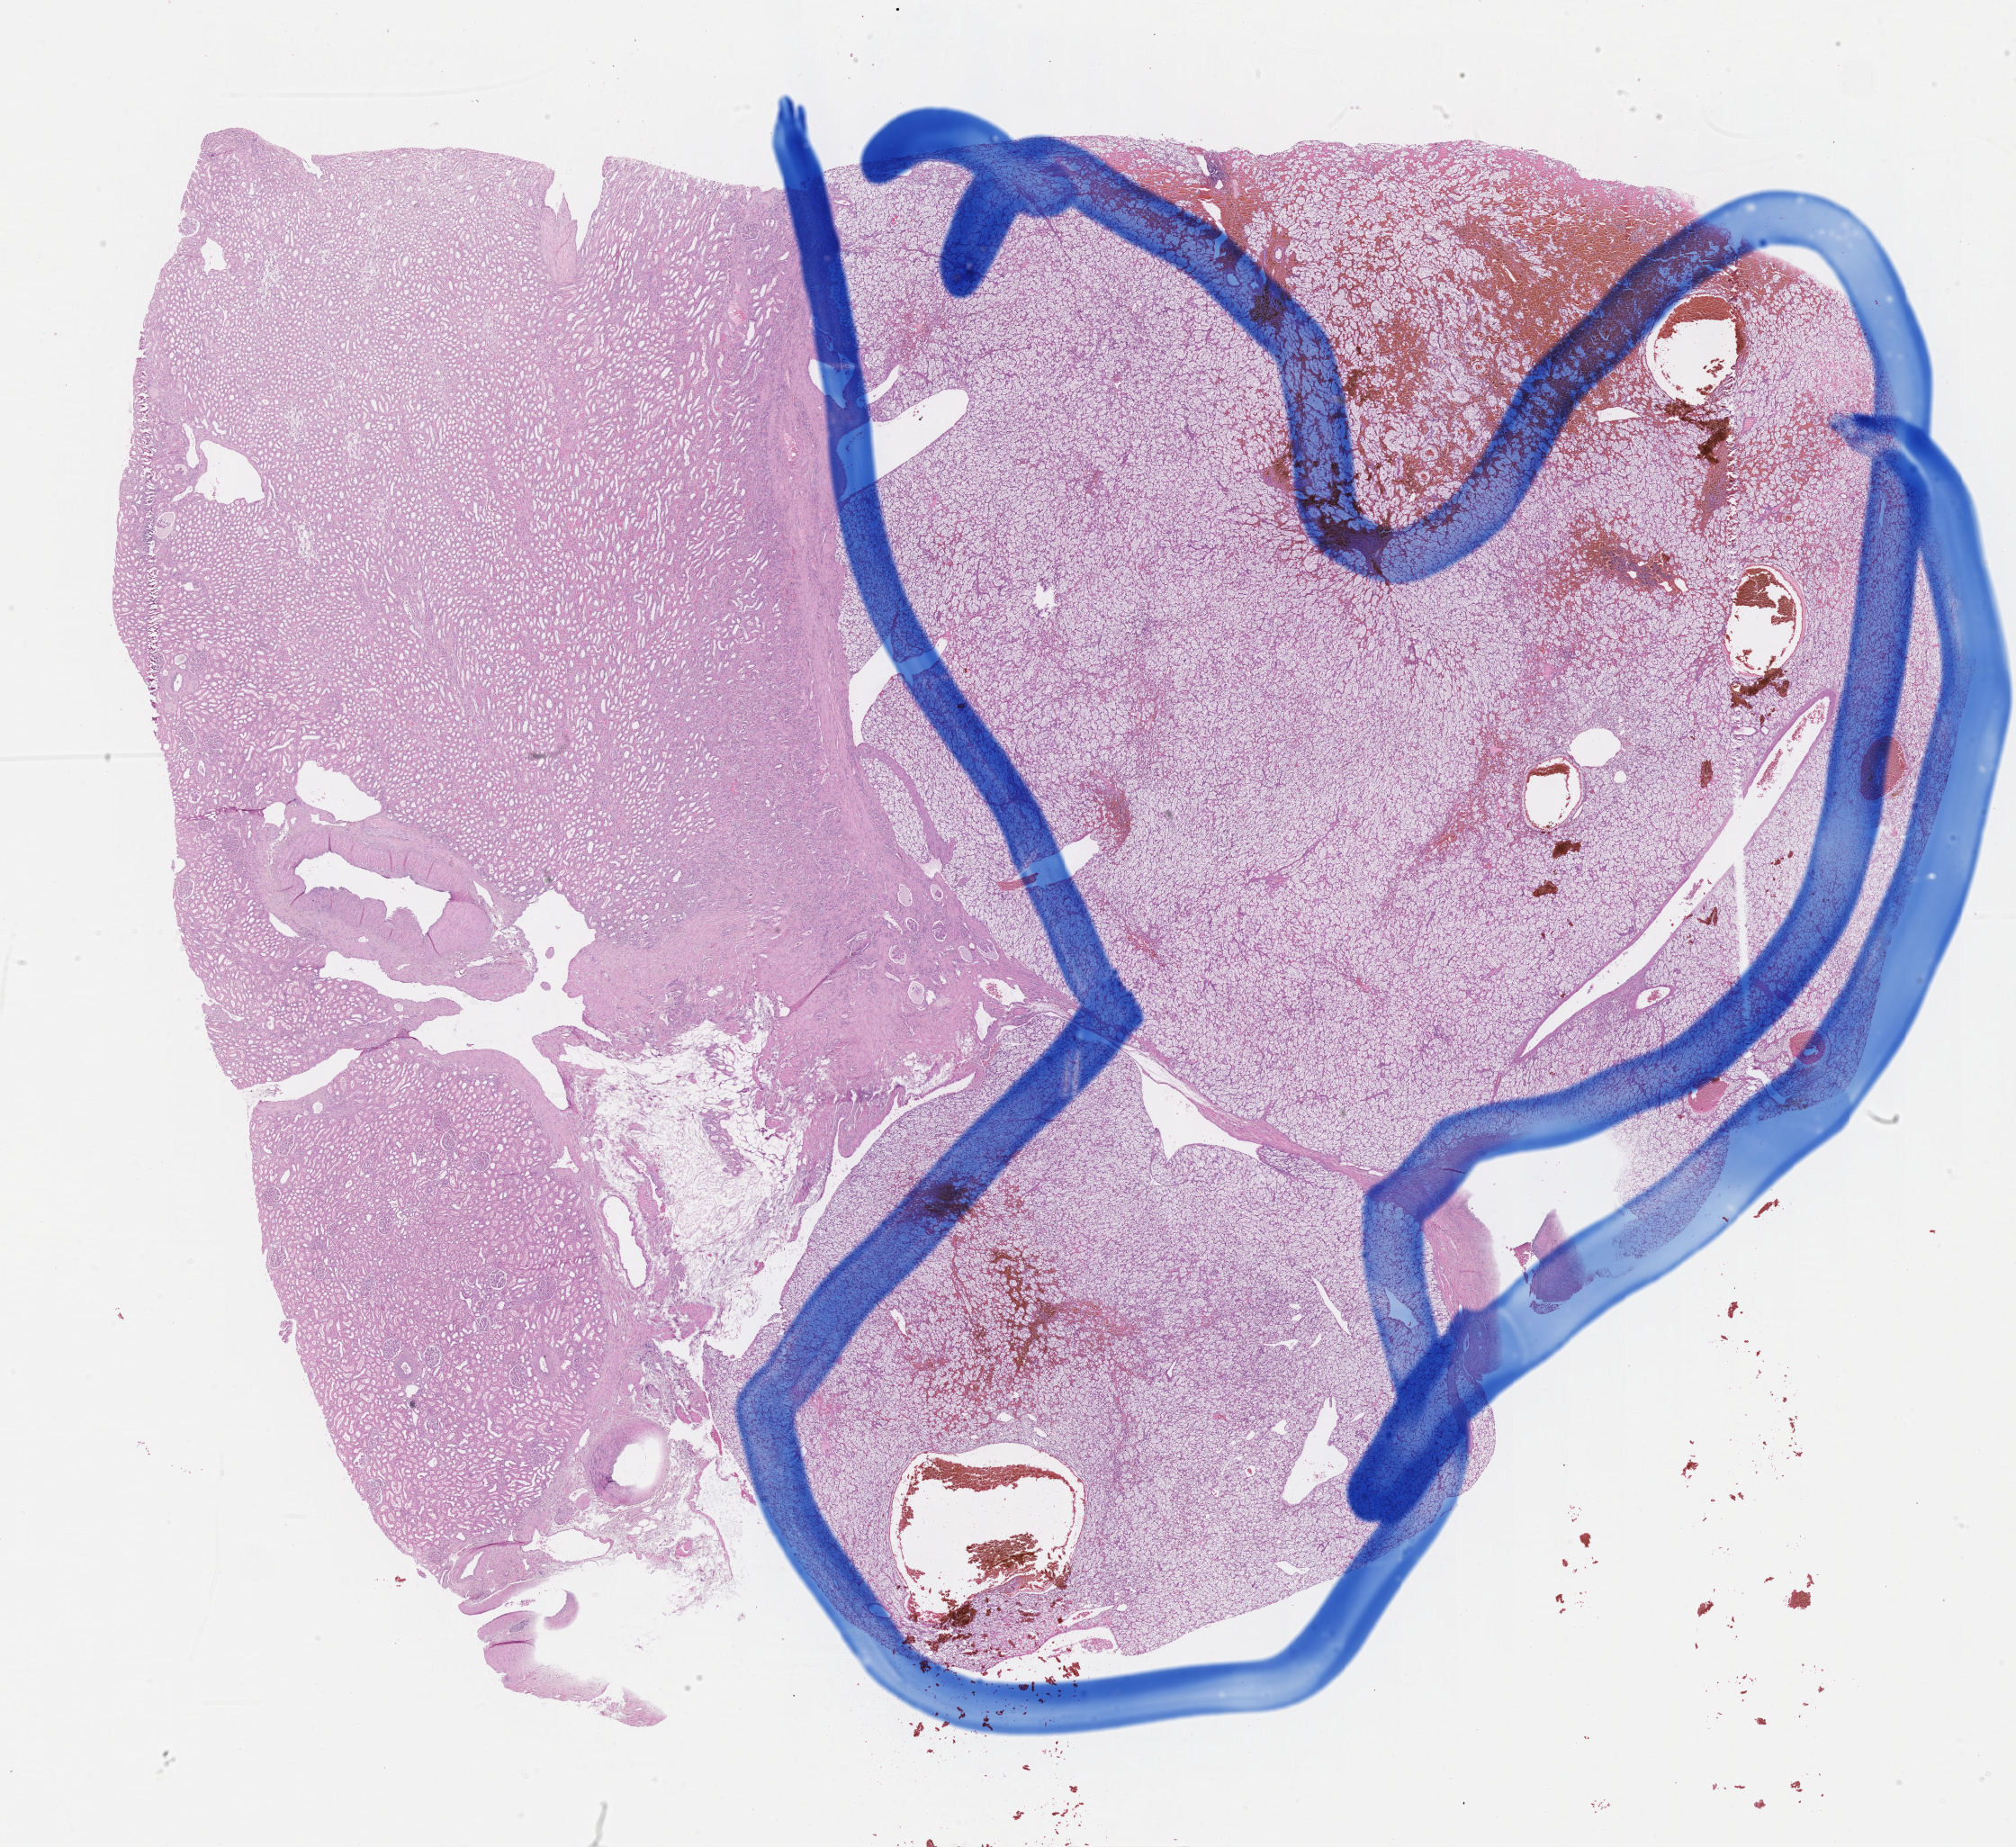
H&E-stained whole-slide image — whole scanned area (about 18.1 x 16.6 mm) shown as a low-resolution overview, formalin-fixed paraffin-embedded (FFPE) diagnostic section, kidney, primary tumour sample. Male, age 42 years at initial diagnosis.
Diagnosis: Clear cell adenocarcinoma, NOS.